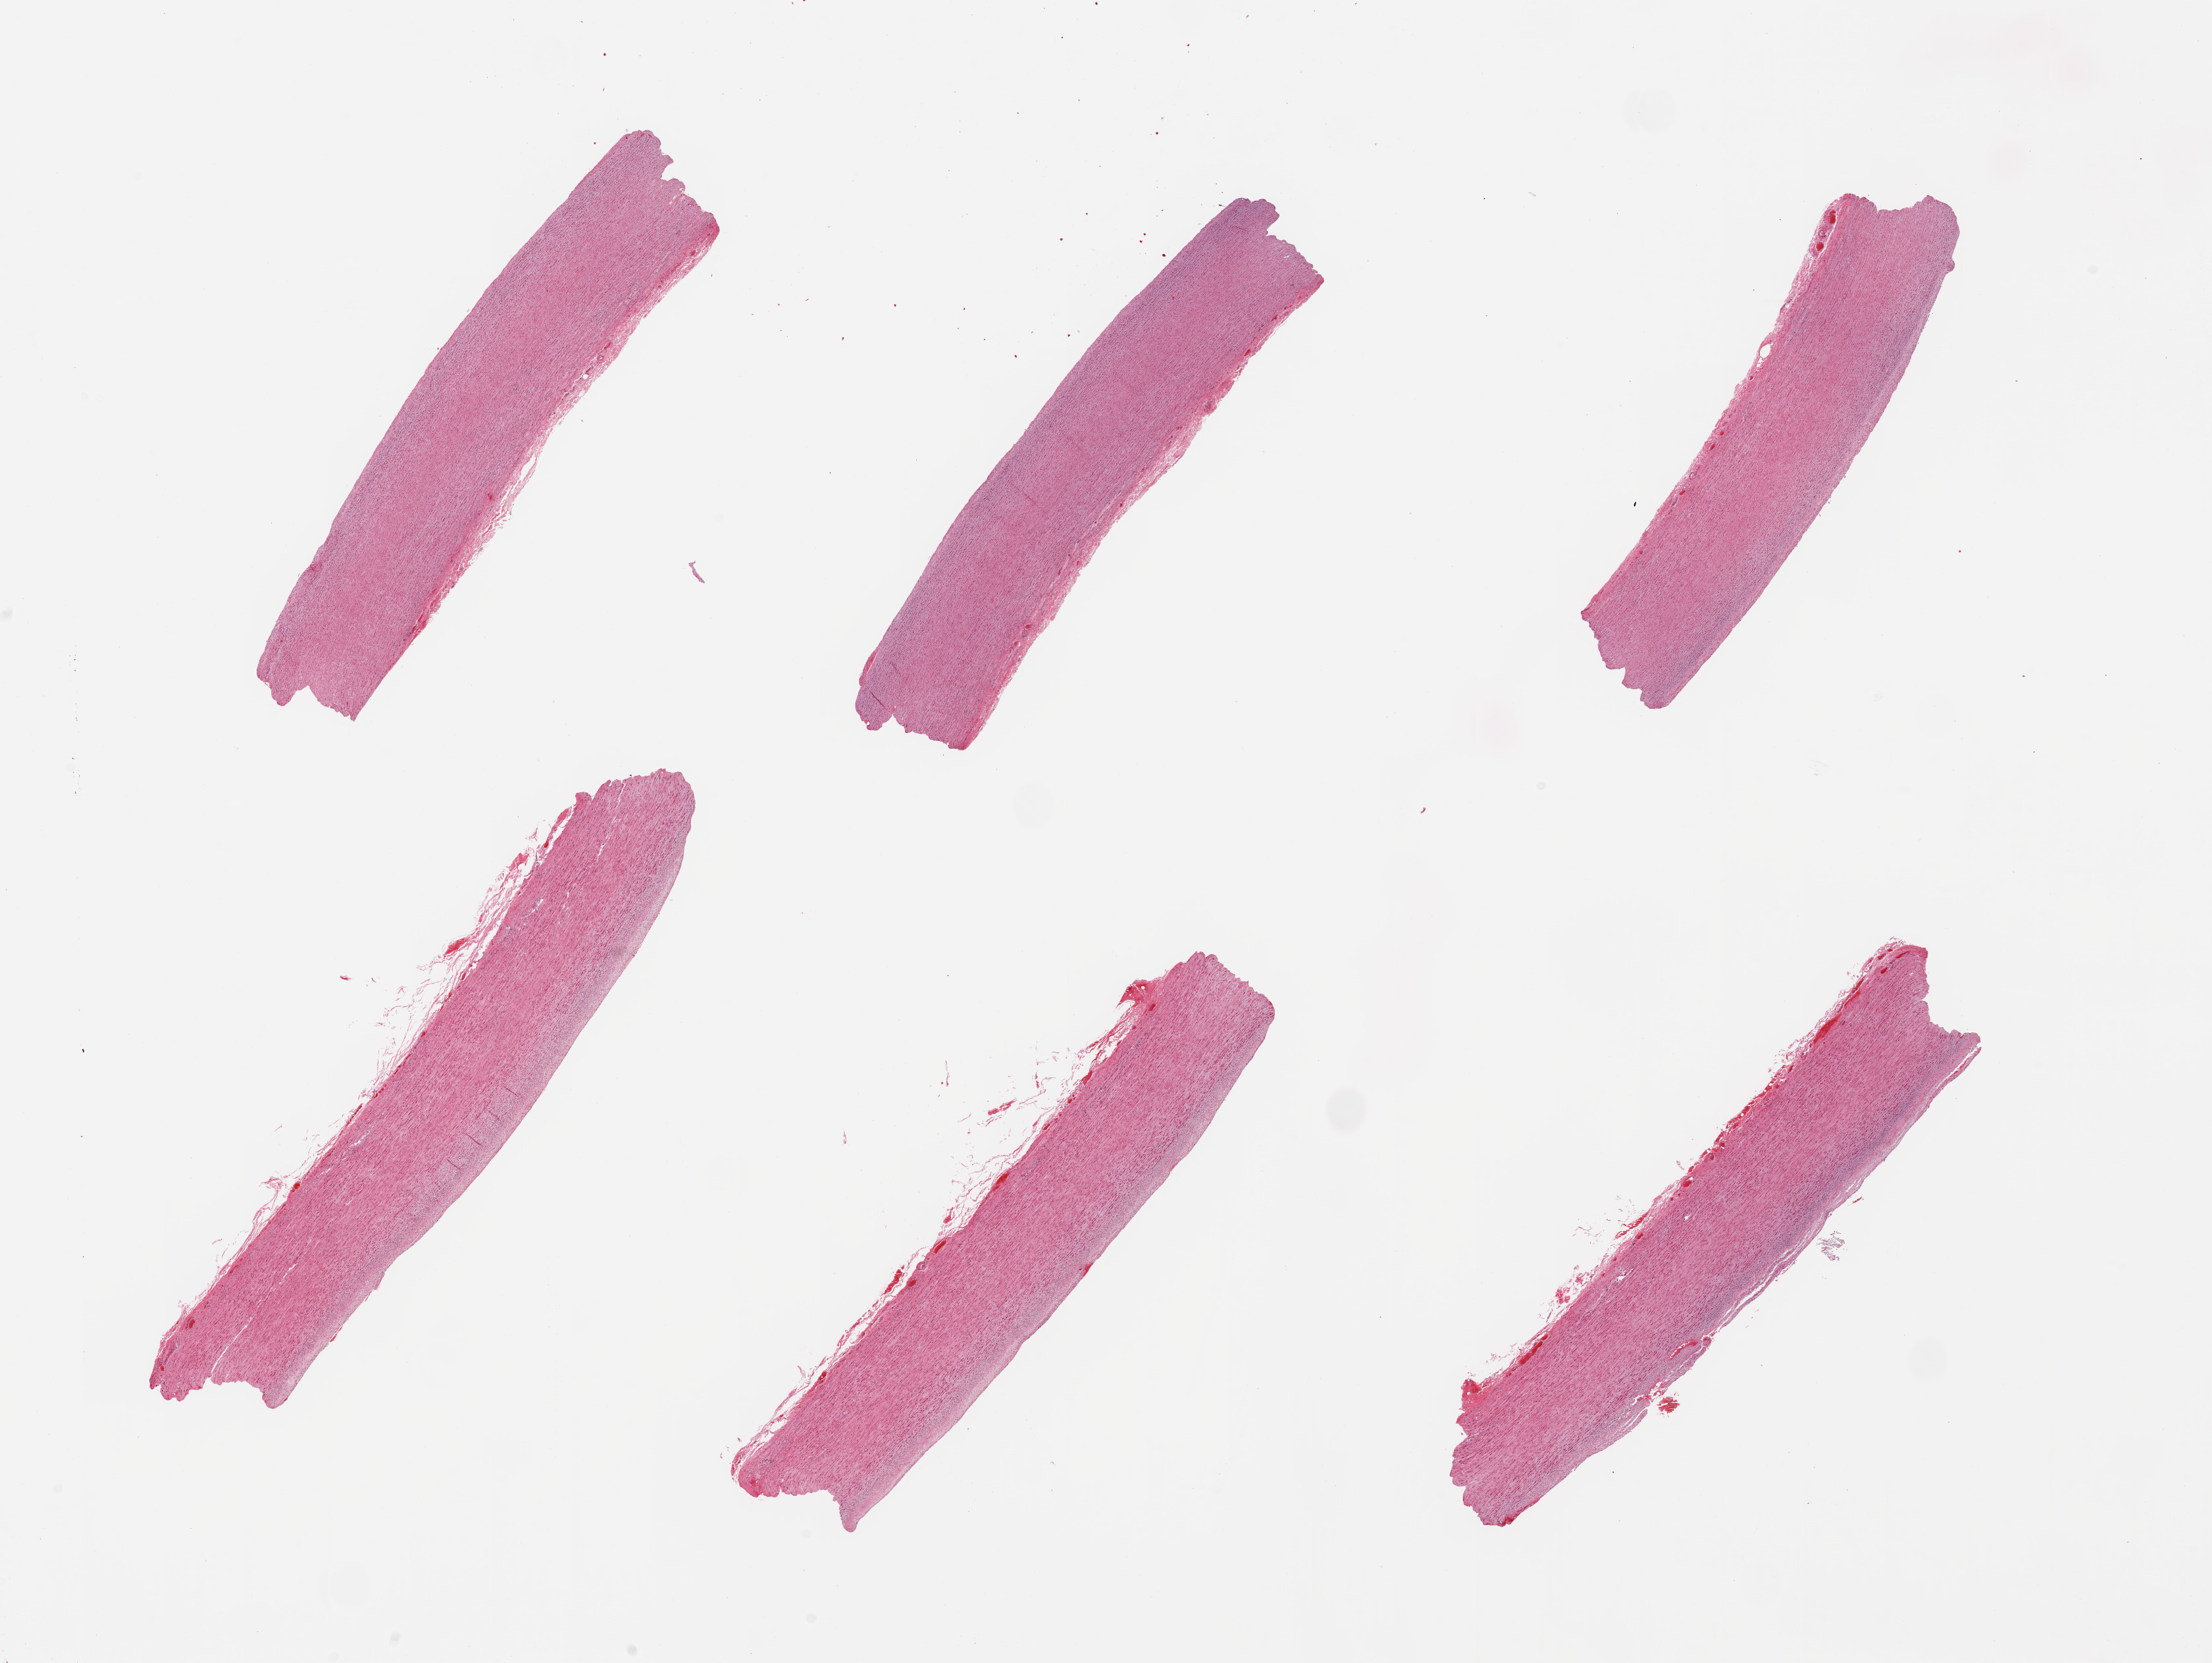
Whole-slide image, haematoxylin and eosin stain, whole scanned area (about 26.6 x 20.0 mm, slide scanned at 20x) shown as a low-resolution overview, PAXgene-fixed, paraffin-embedded tissue, target tissue: aorta, donor tissue sample. Donor: male.
Pathologist's review note for this sample: 6 pieces; well trimmed and with atheromatous plaque formation.